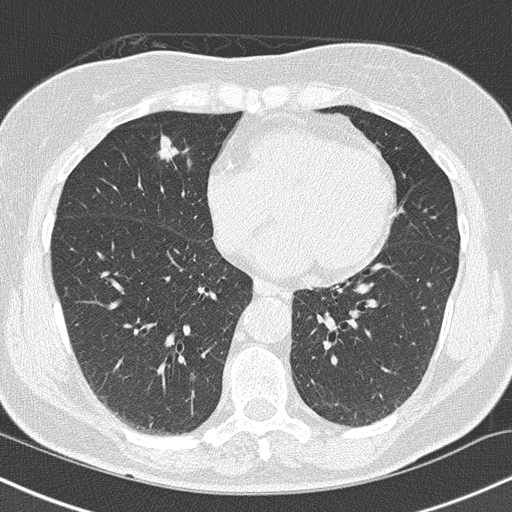
Axial slice from a low-dose chest CT screening exam. Baseline annual screen. Lung window (W 1500 / L -600 HU). 2 mm slice thickness. Lung (sharp) reconstruction kernel (B50f). Female participant, aged 66 years at enrolment.
- Expert-annotated lung lesion, bounding box <145,129,182,165> (left, top, right, bottom; pixels).
- Reader record for this screening exam (exam-level; its link to the box is not recorded): non-calcified nodule or mass ≥4 mm, right lower lobe, 10 × 8 mm, smooth margins, soft tissue attenuation.
- Official screen result: positive, change unspecified: nodule(s) >= 4 mm or enlarging nodule(s), mass(es), or other non-specific abnormalities suspicious for lung cancer.
- Later outcome: lung cancer diagnosed 96 days after this screen — squamous cell carcinoma, keratinizing, NOS, right upper lobe, right middle lobe, poorly differentiated (G3), stage IA (AJCC 6th edition), 14 mm at pathology.